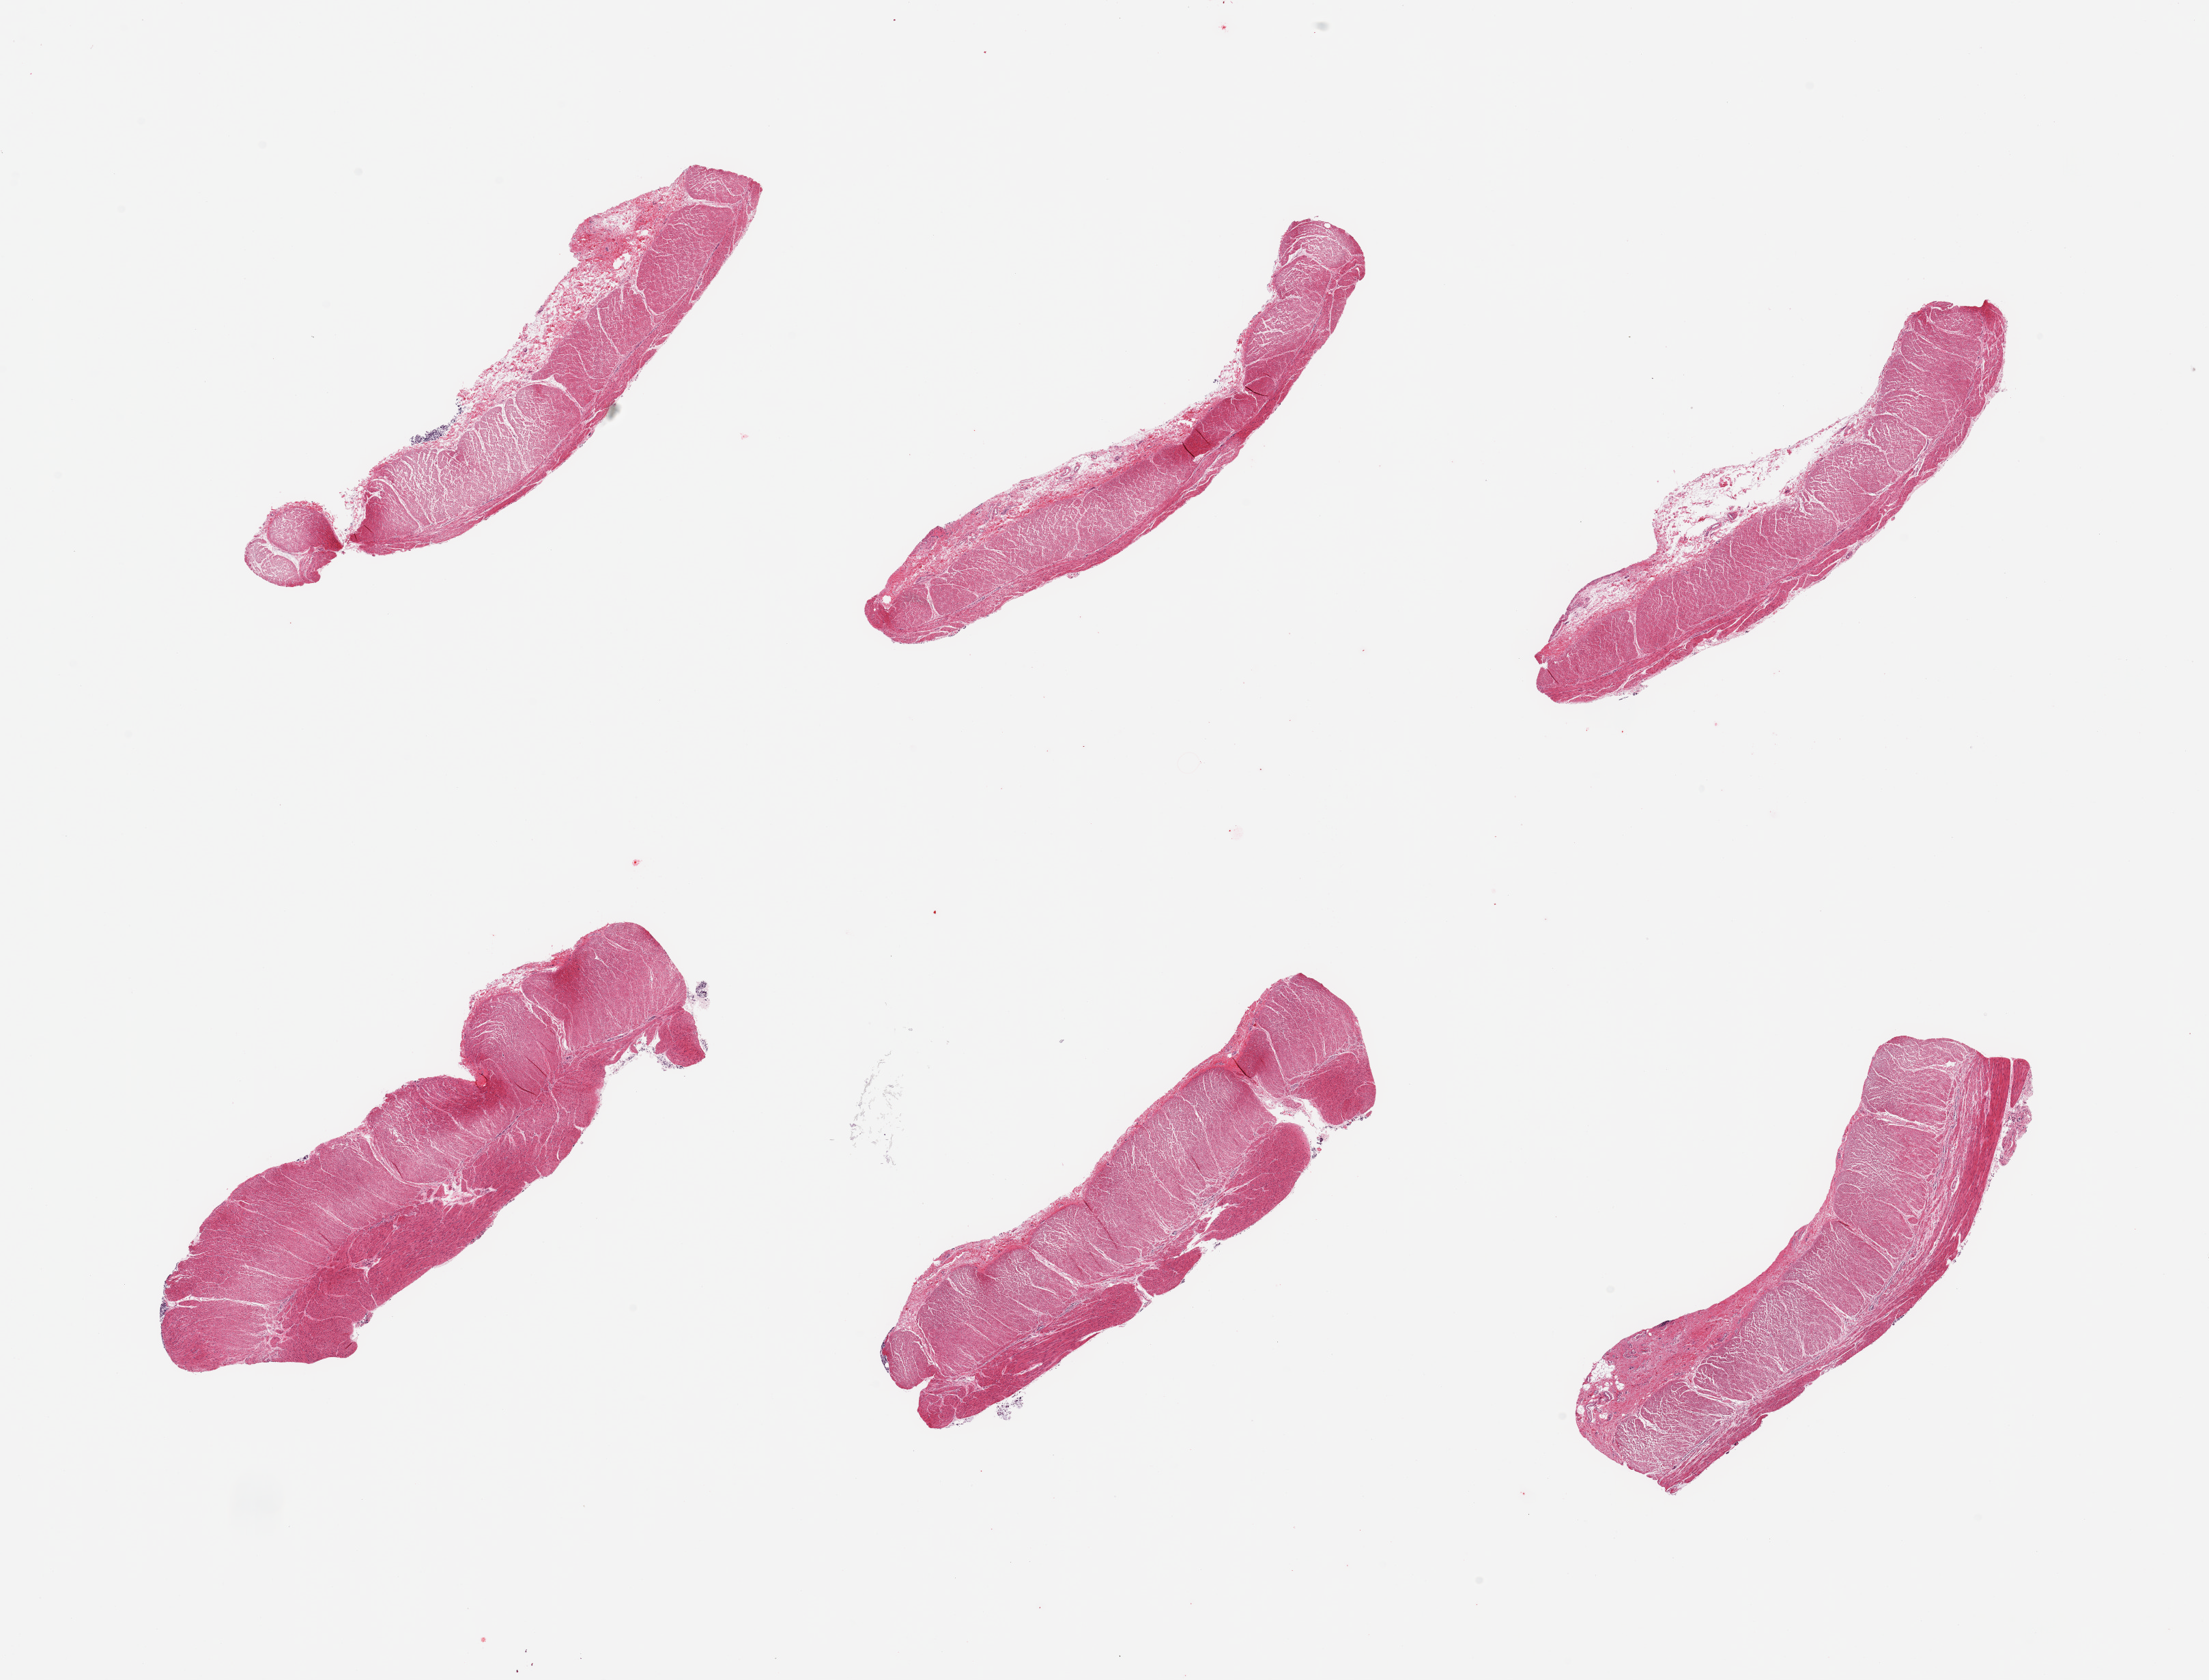
Whole-slide image, haematoxylin and eosin stain — shown as a low-resolution overview of the whole scanned area (about 25.6 x 19.5 mm). PAXgene-fixed, paraffin-embedded tissue. Section of sigmoid colon (target tissue). Tissue donor sample. Donor: female.
- pathologist's review note for this sample: 6 pieces; well dissected muscularis